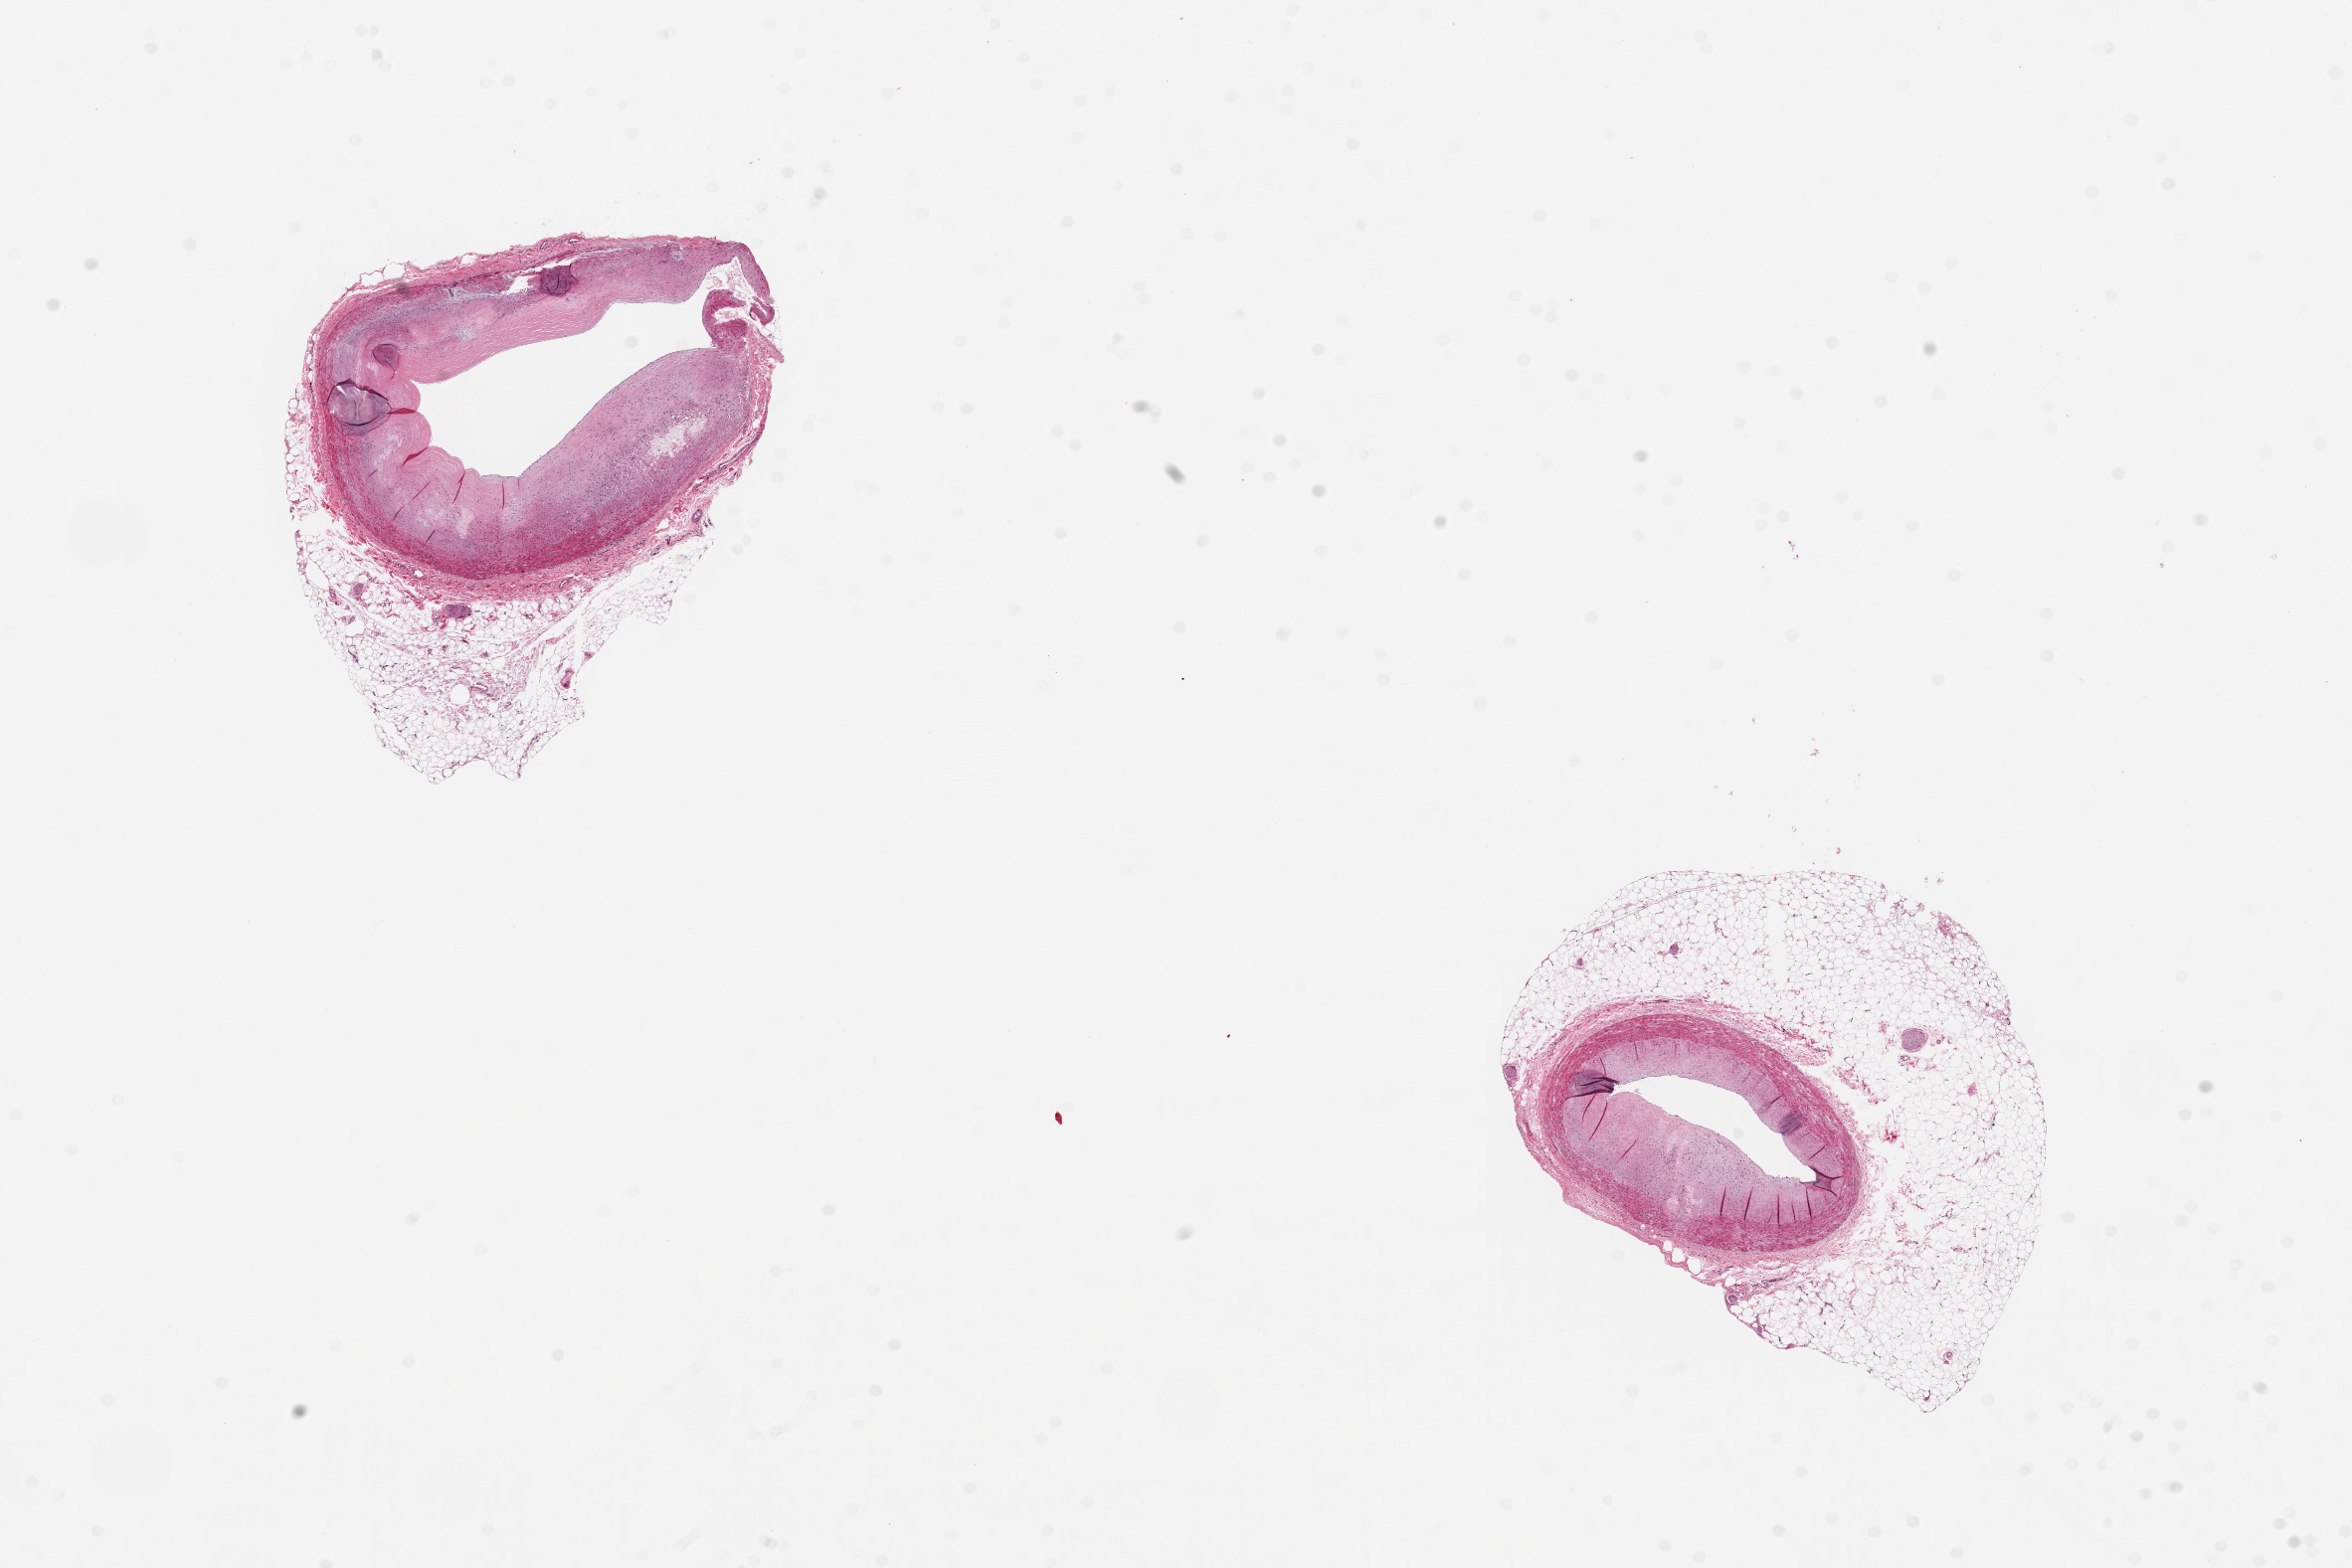
Digitized H&E-stained section, brightfield — low-resolution overview of the scanned area, about 18.7 x 12.5 mm, PAXgene-fixed, paraffin-embedded tissue, target tissue: coronary artery, tissue donor sample. Male donor.
* reviewer comment on this tissue sample: 2 ~3.5mm d pieces, ~40% occlusive atherosclerosis